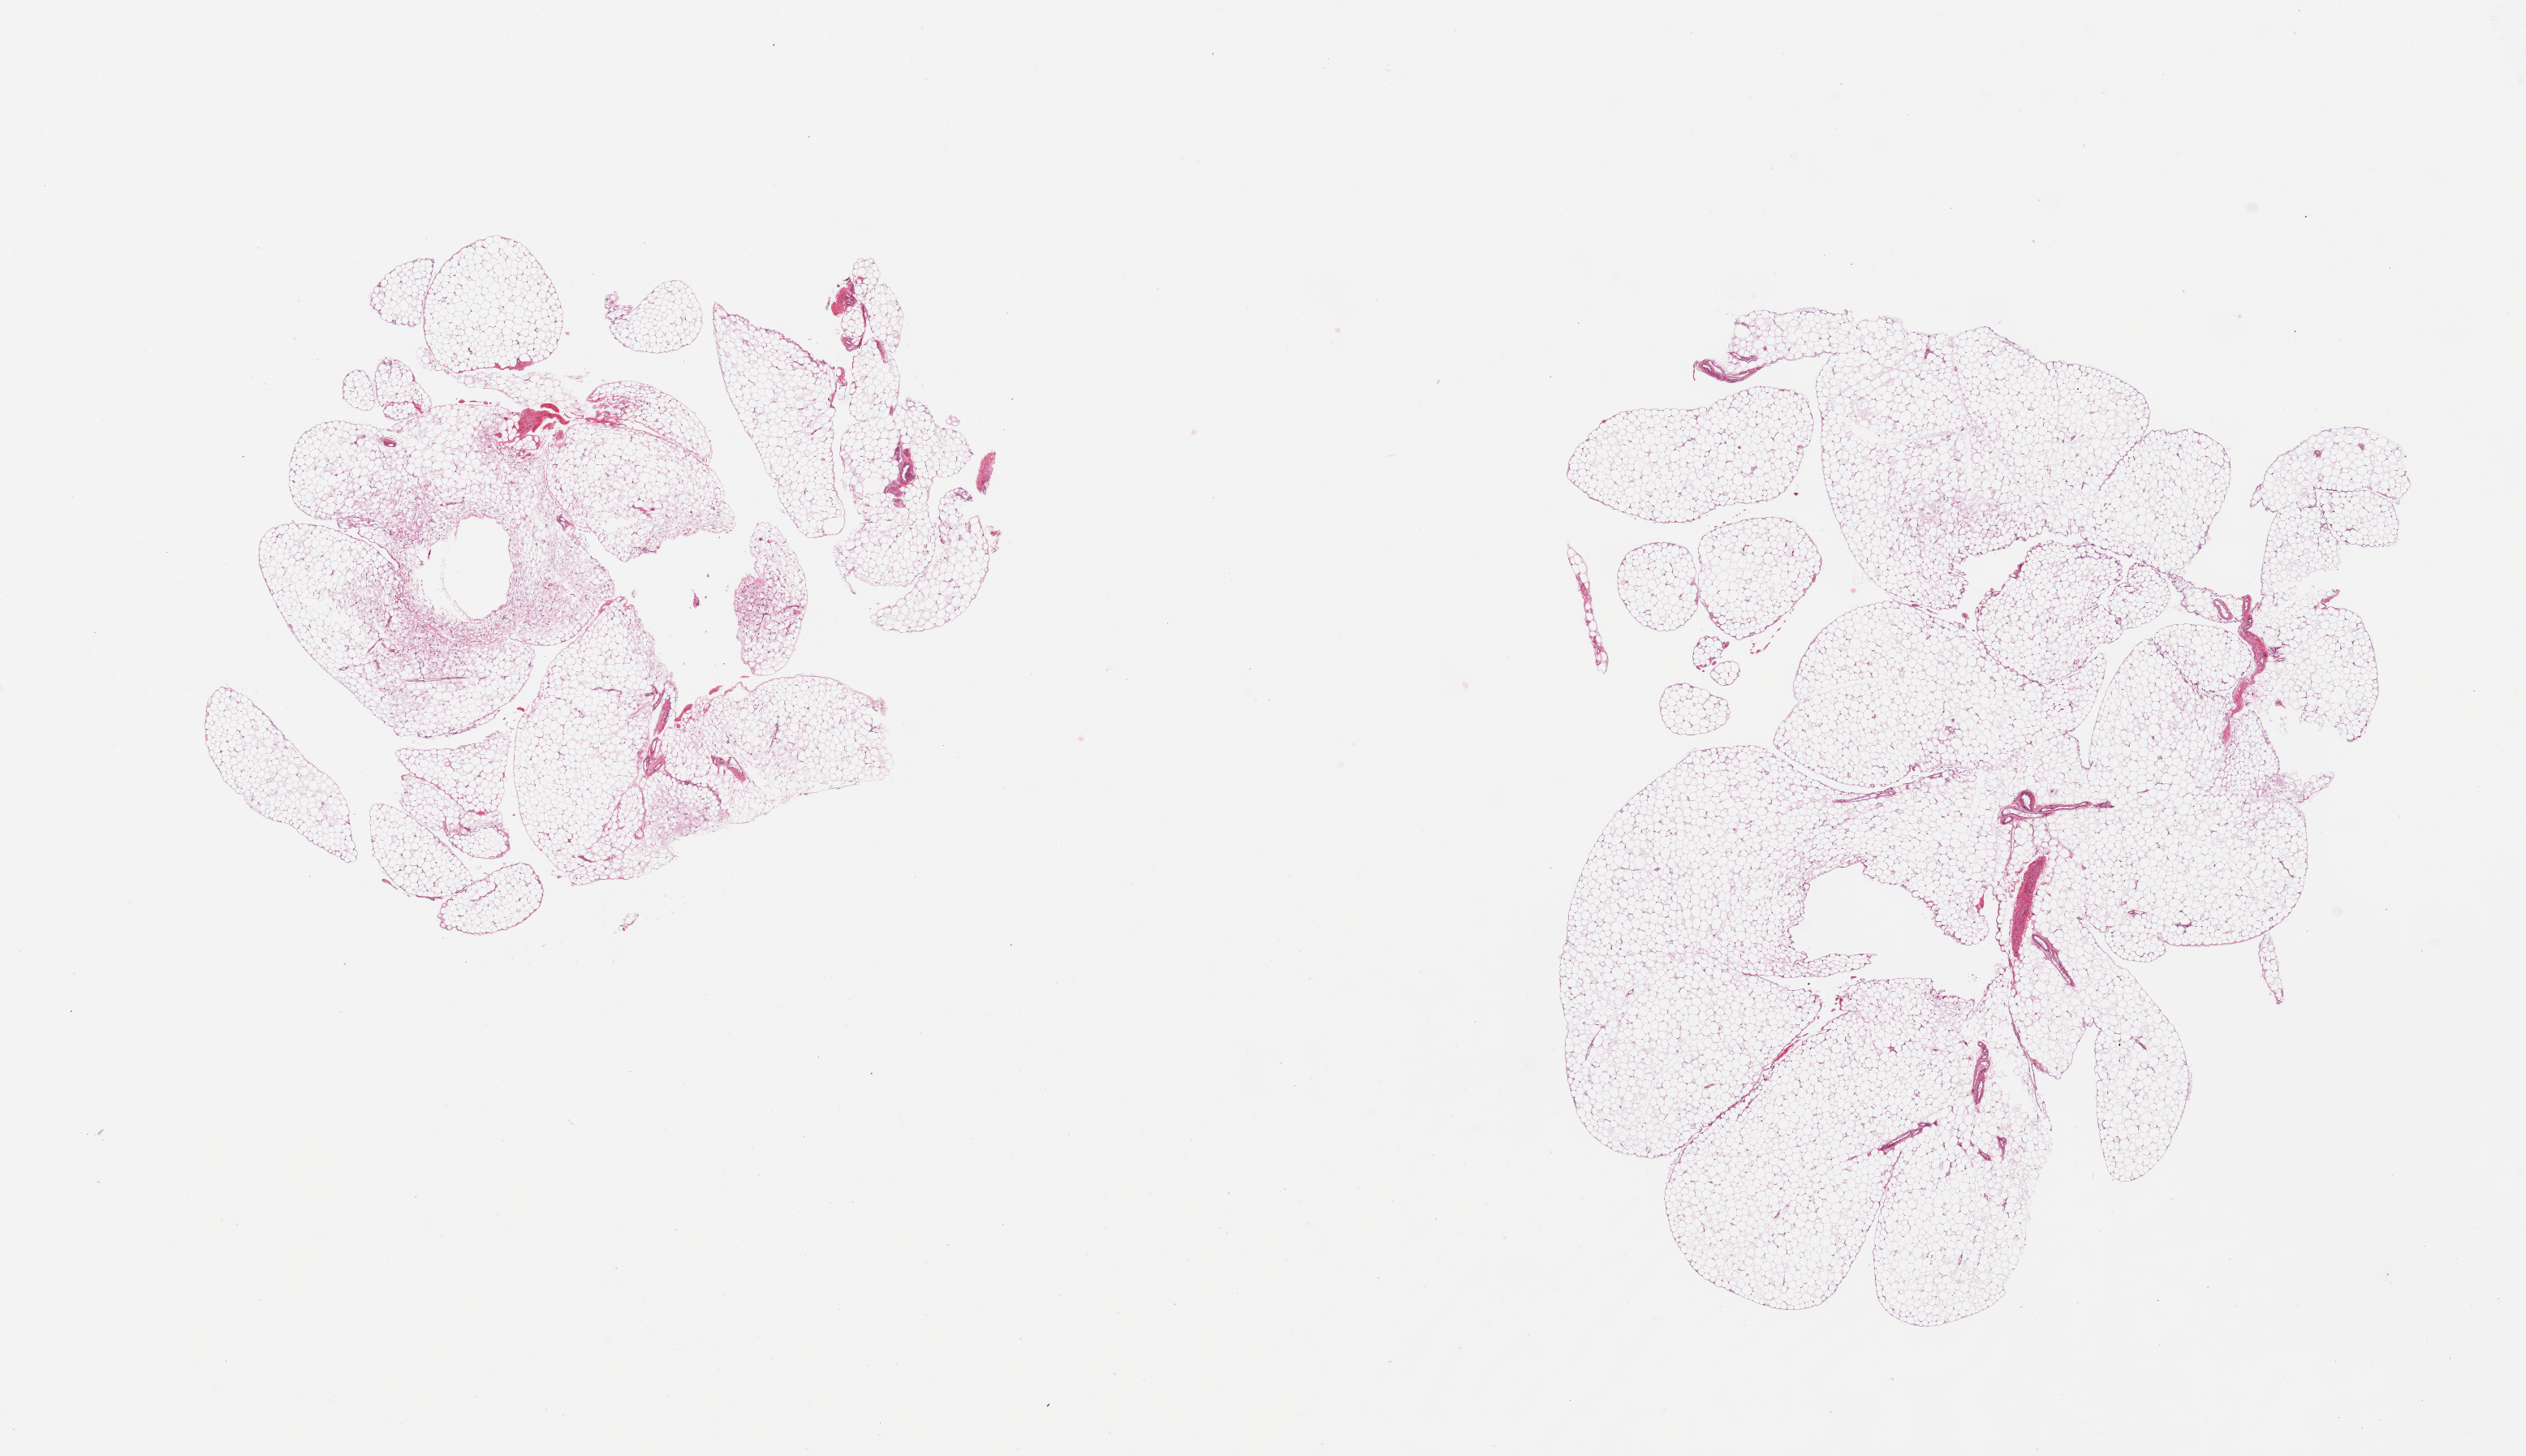
Whole-slide image, H&E stain, whole scanned area (about 24.6 x 14.2 mm) shown as a low-resolution overview. PAXgene-fixed paraffin-embedded (PFPE) section. Target tissue: omentum. Tissue donor sample.
• pathologist's review note for this sample: 2 pieces; lobulated mature fat